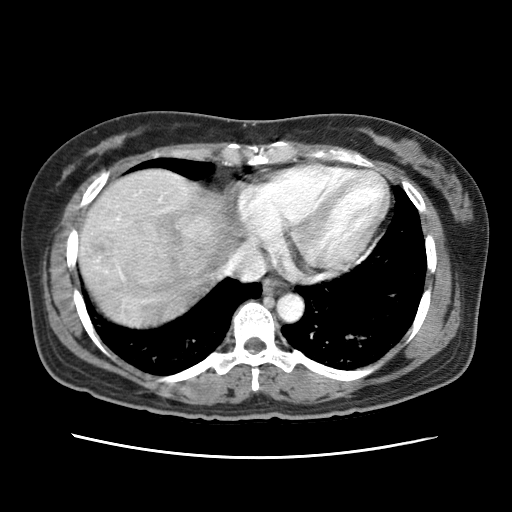
Contrast-enhanced abdominal CT (liver protocol), one axial slice. Reconstruction kernel STANDARD. 120 kVp. Soft-tissue window (W 400 / L 40 HU). 2.5 mm slice thickness. 512 × 512 image matrix, field of view 340 × 340 mm. Case-level facts recorded for this patient, not image findings: diagnosis: hepatocellular carcinoma (patient treated with transarterial chemoembolisation; whether this scan precedes or follows treatment is not stated here); TNM stage (as recorded): Stage-I; Child-Pugh class: A; tumour differentiation: moderately differentiated; tumour nodularity: uninodular.
Annotated regions visible in this slice (semi-automatic segmentation, software-assisted and operator-edited):
- abdominal aorta: bounding box <276,293,303,321> (left, top, right, bottom; pixels)
- liver parenchyma outside the tumour (the mass and vessels are separate outlines, so this box may not span the whole liver): <78,170,222,326>
- mass: <114,205,217,292>
- liver vessels: <117,175,178,220>